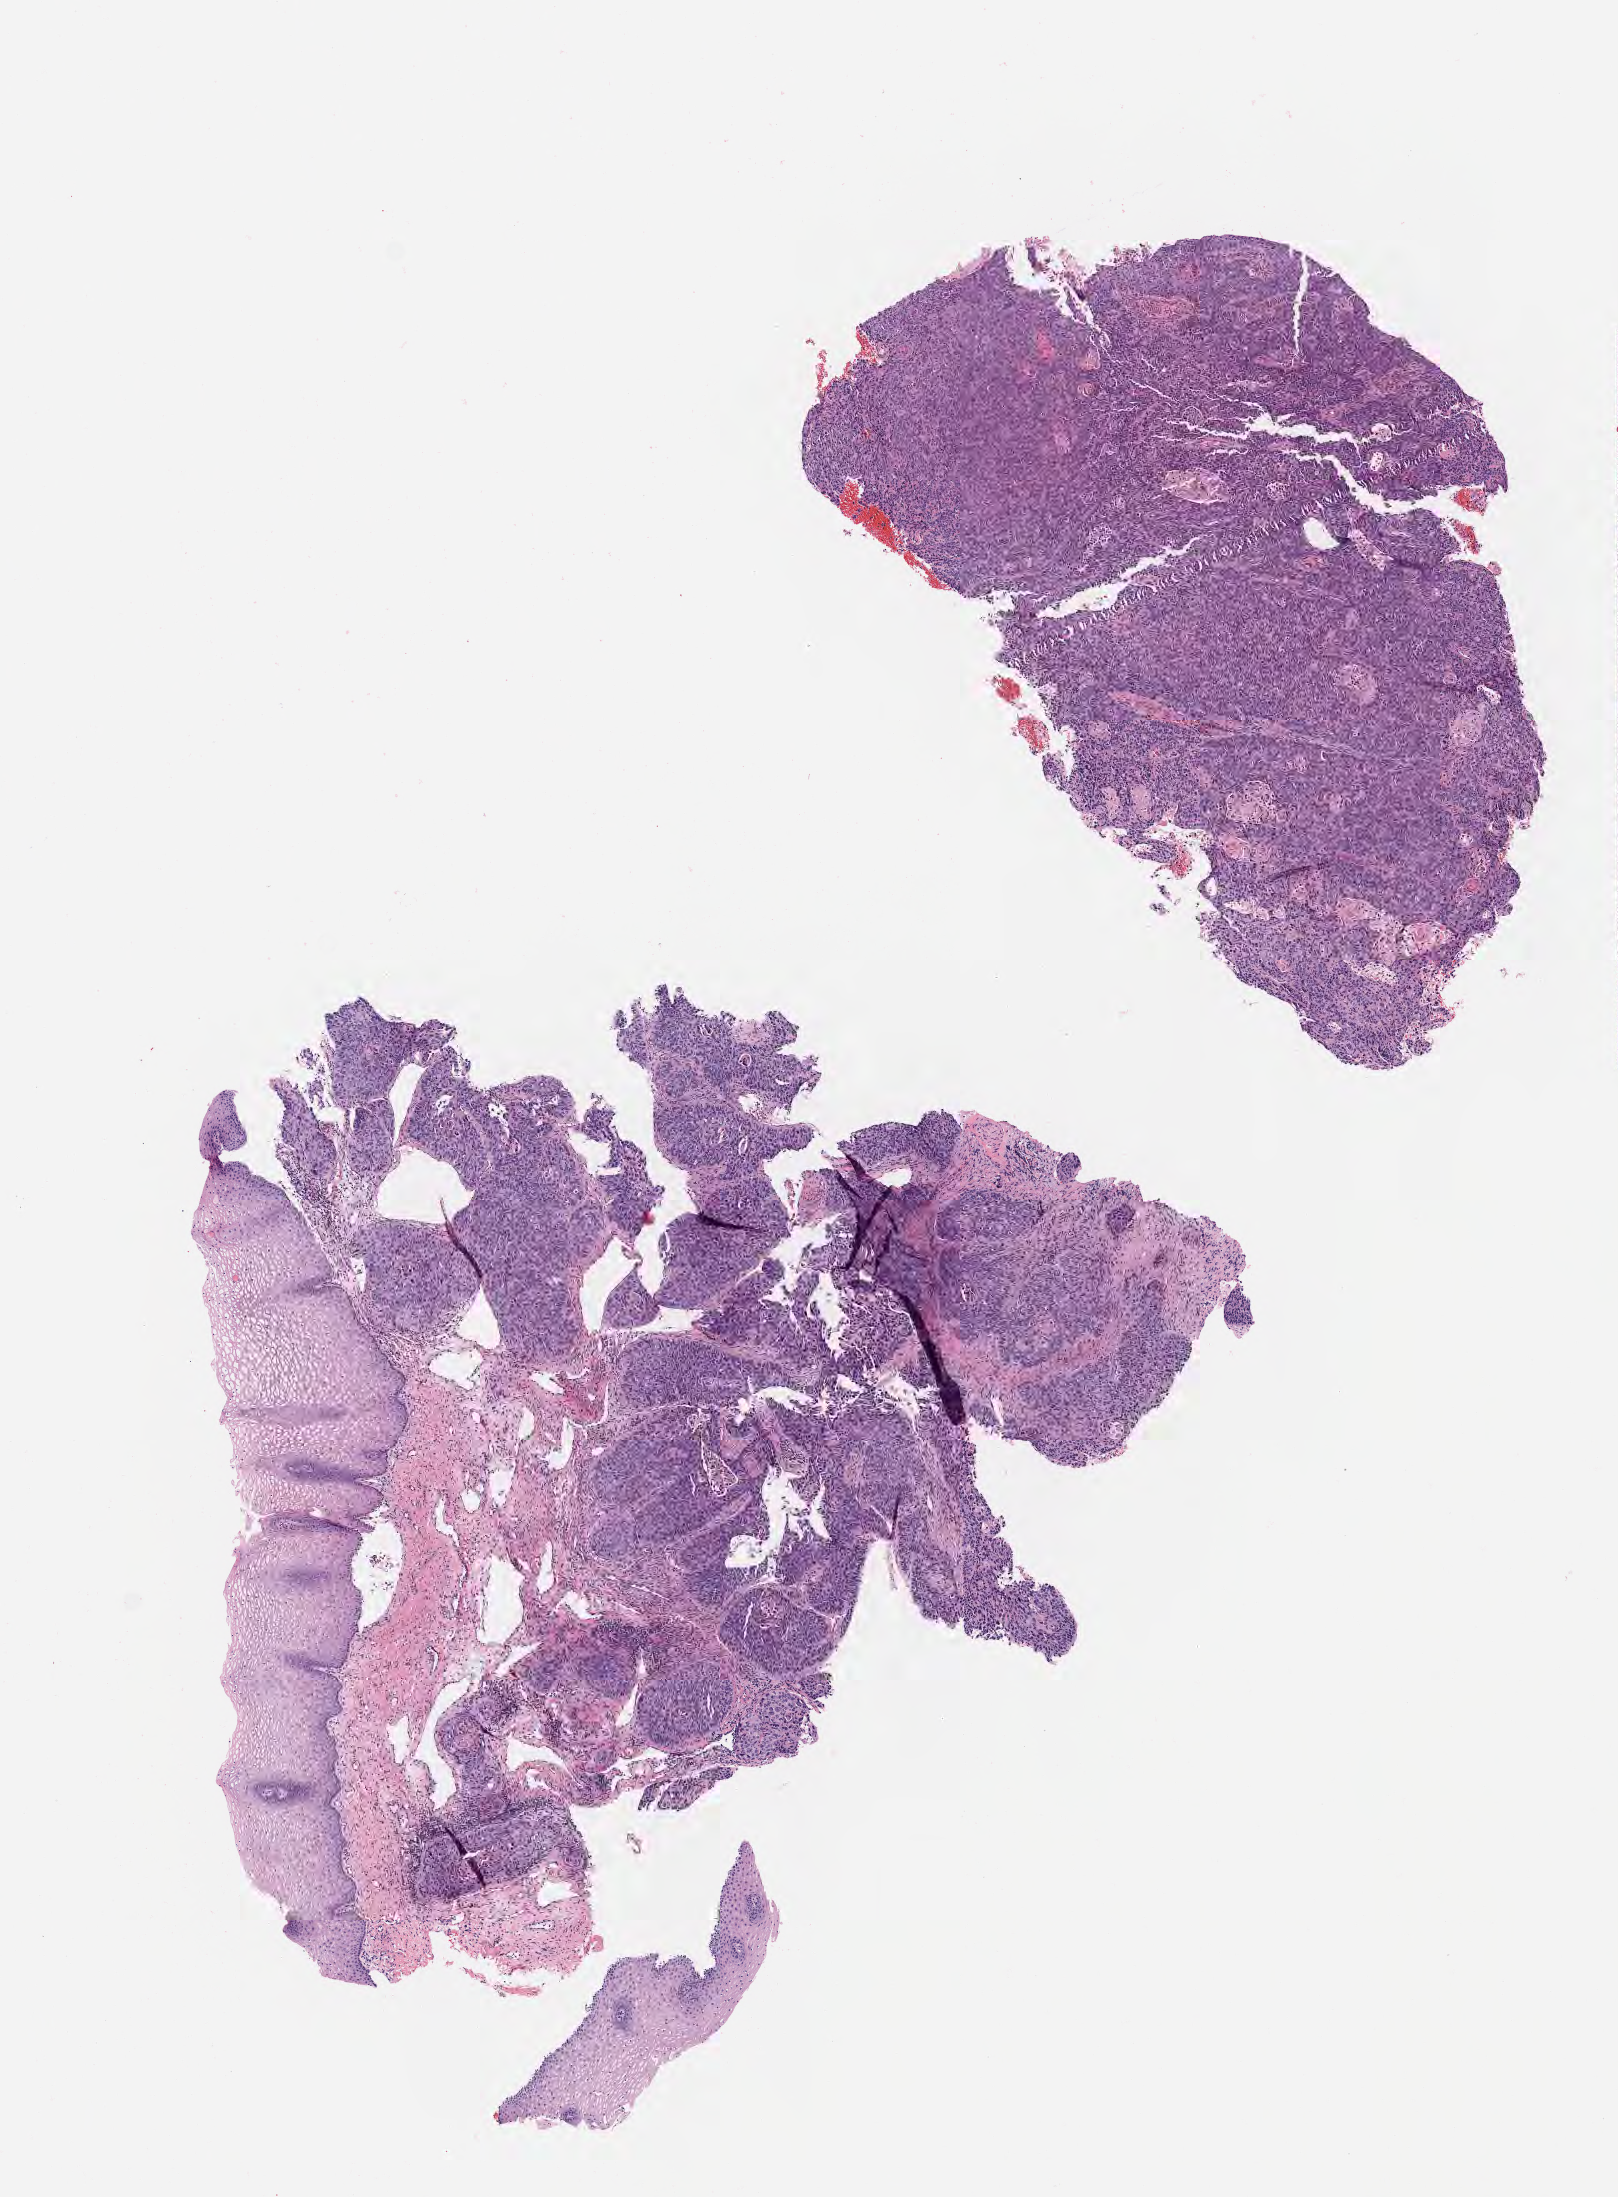
Digitized haematoxylin and eosin-stained section — shown as a low-resolution overview of the whole scanned area (about 6.5 x 8.9 mm), tumor tissue, site: cervix. Patient female; 35 years old.
Diagnosis: Squamous cell carcinoma, keratinizing, NOS.